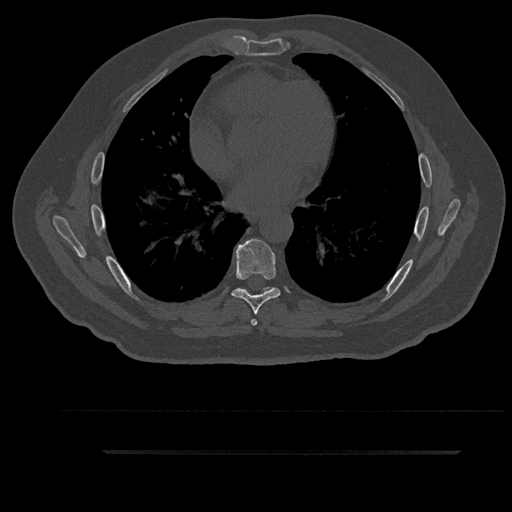
CT including the spine, one axial slice; slice 522 of 797 in the series (ordered by position); reconstruction kernel Br40s/3; bone window (W 1800 / L 400 HU); 0.5 mm slice thickness; 512 × 512 image matrix, field of view 432 × 432 mm. Male patient, age 63 years. Case-level facts recorded for this patient, not image findings: primary cancer: renal; vertebrae with lytic lesions (as recorded): T8.
Annotated regions visible in this slice (semi-automatically segmented with operator editing):
- T6 vertebra: bounding box <241,288,271,326> (left, top, right, bottom; pixels)
- T7 vertebra: <231,239,281,315>
- T8 vertebra: <242,286,272,291>